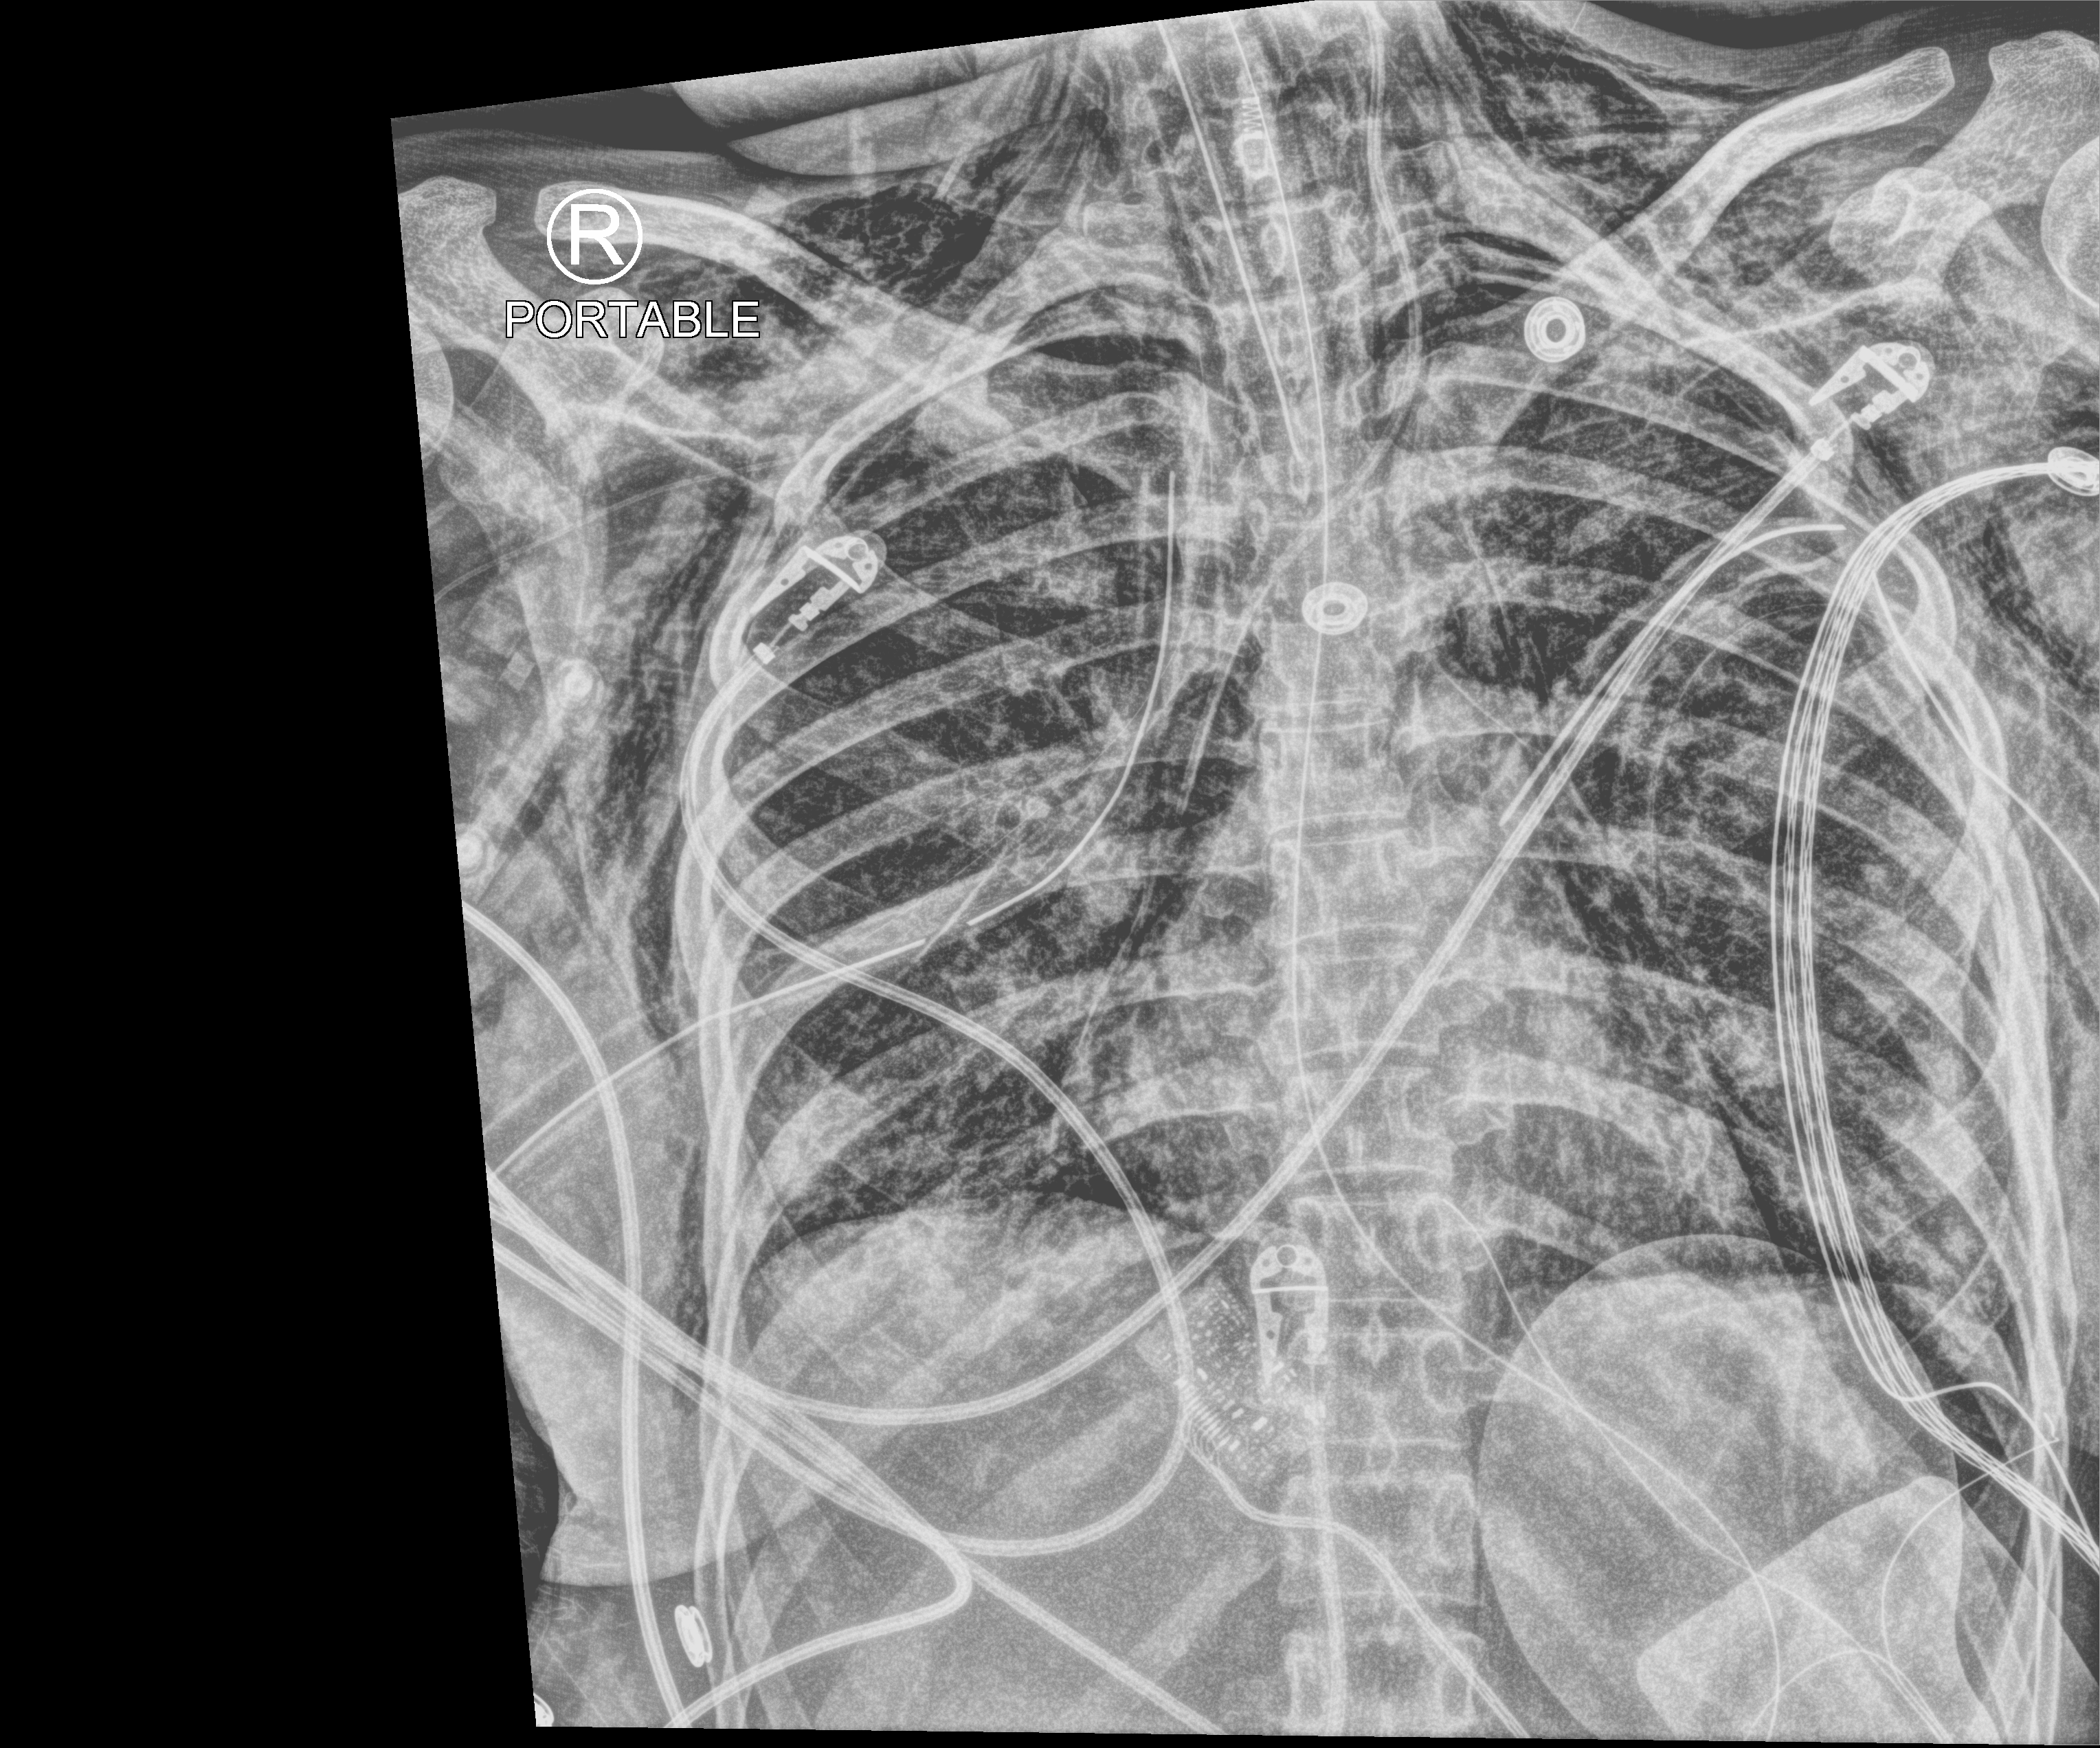
Bedside chest radiograph (computed radiography), anteroposterior (AP) projection. Patient hospitalised with COVID-19, aged 18–59 years.
Admission-level facts for this patient (not findings on this image; timing relative to this image not recorded):
- hypertension (admission record): no
- mechanically ventilated during this hospital stay: yes
- admitted to intensive care during this hospital stay: yes